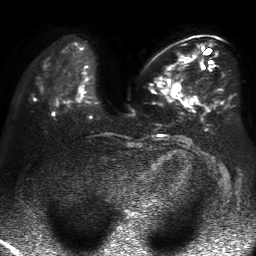
Breast MRI, one axial slice. Position 20 of 50 along the scan axis. Diffusion-weighted series; image 2 of 4 stored at this slice position (different b-values; order by instance number). 1.5 T. 4 mm slice thickness. 256 × 256 image matrix, field of view 360 × 360 mm. Female patient.
Outlined on this slice (outlined manually by an expert reader):
- tumour on diffusion-weighted imaging: bounding box [x1, y1, x2, y2] px = [174, 53, 184, 91]